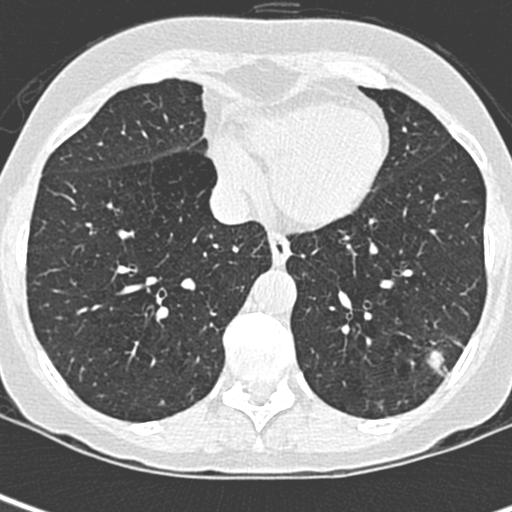
Low-dose screening chest CT, one axial slice; slice 93 of 252 in the series (ordered by position); 120 kVp; lung window (W 1500 / L -600 HU); 1.3 mm slice thickness; 512 × 512 image matrix.
Annotated regions visible in this slice (expert manual segmentation):
- lesion 1 (tumor, lower lobe of left lung): bounding box (x1, y1, x2, y2) in pixels: (427, 350, 448, 377)